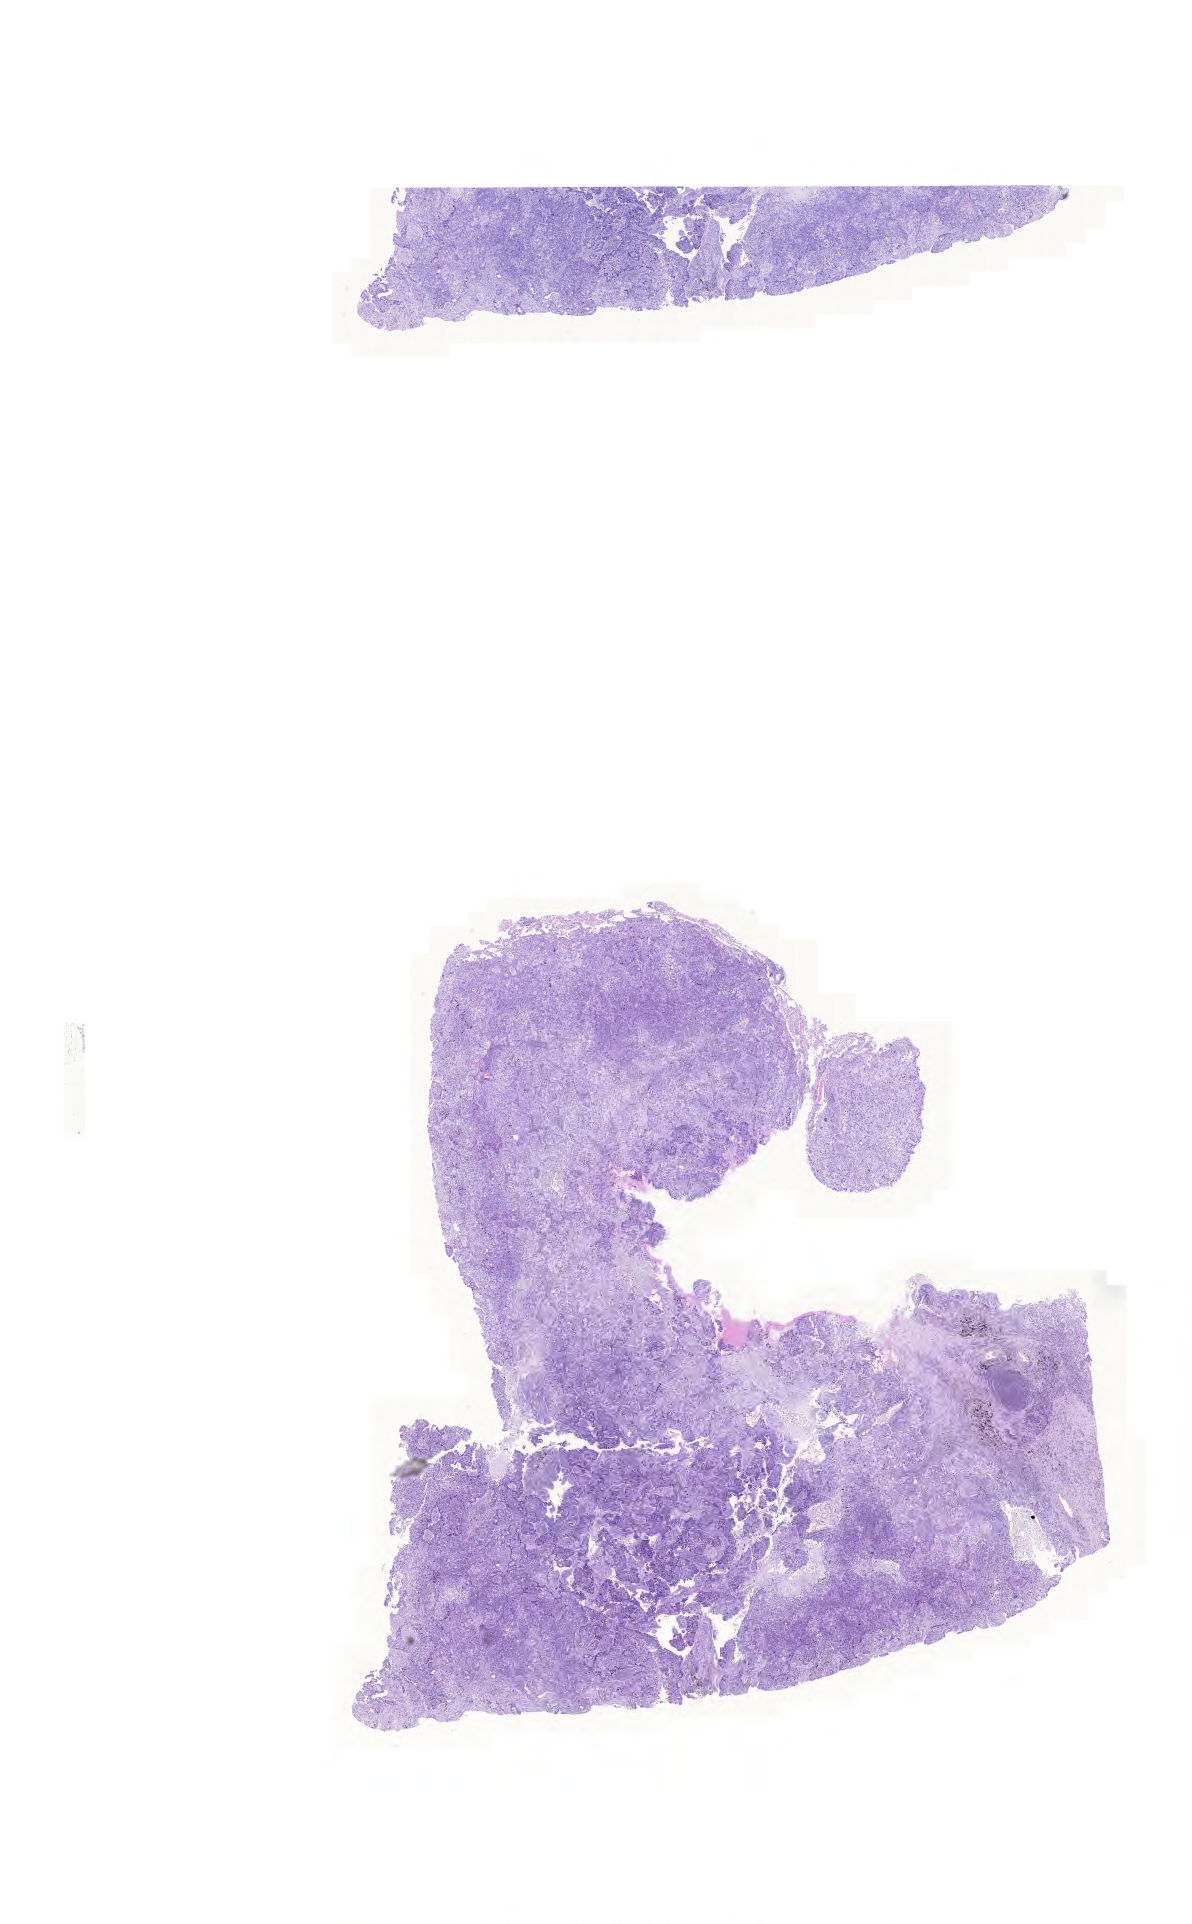
Whole-slide histology image, H&E, a low-resolution overview of the entire scanned area, about 17.7 x 28.6 mm. FFPE section. Lung, primary tumour sample. Female patient; age at initial diagnosis 65 years.
Histologic diagnosis: Adenocarcinoma with mixed subtypes (upper lobe, lung).